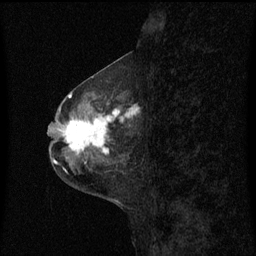
Breast MRI (dynamic contrast-enhanced), one sagittal slice. Slice 26 of 60 in the series (ordered by position). Dynamic contrast-enhanced series, image 2 of 3 at this slice position (ordered by acquisition). 1.5 T. TE 4.2 ms, TR 8.4 ms. 2 mm slice thickness. 256 × 256 image matrix, field of view 200 × 200 mm. Patient: female, 49 years. Case-level facts recorded for this patient, not image findings: setting: breast cancer imaged before/during neoadjuvant chemotherapy; receptor status: HR-positive, HER2-negative.
Structures marked on this image (semi-automatically segmented with operator editing):
- analysis volume of interest (the breast-tissue region the enhancement analysis was run in; not a lesion): bounding box (x1, y1, x2, y2) in pixels: (59, 101, 138, 158)
- tumour enhancement mask (voxels above the 70 % enhancement threshold inside the analysis volume of interest): (66, 109, 137, 154)